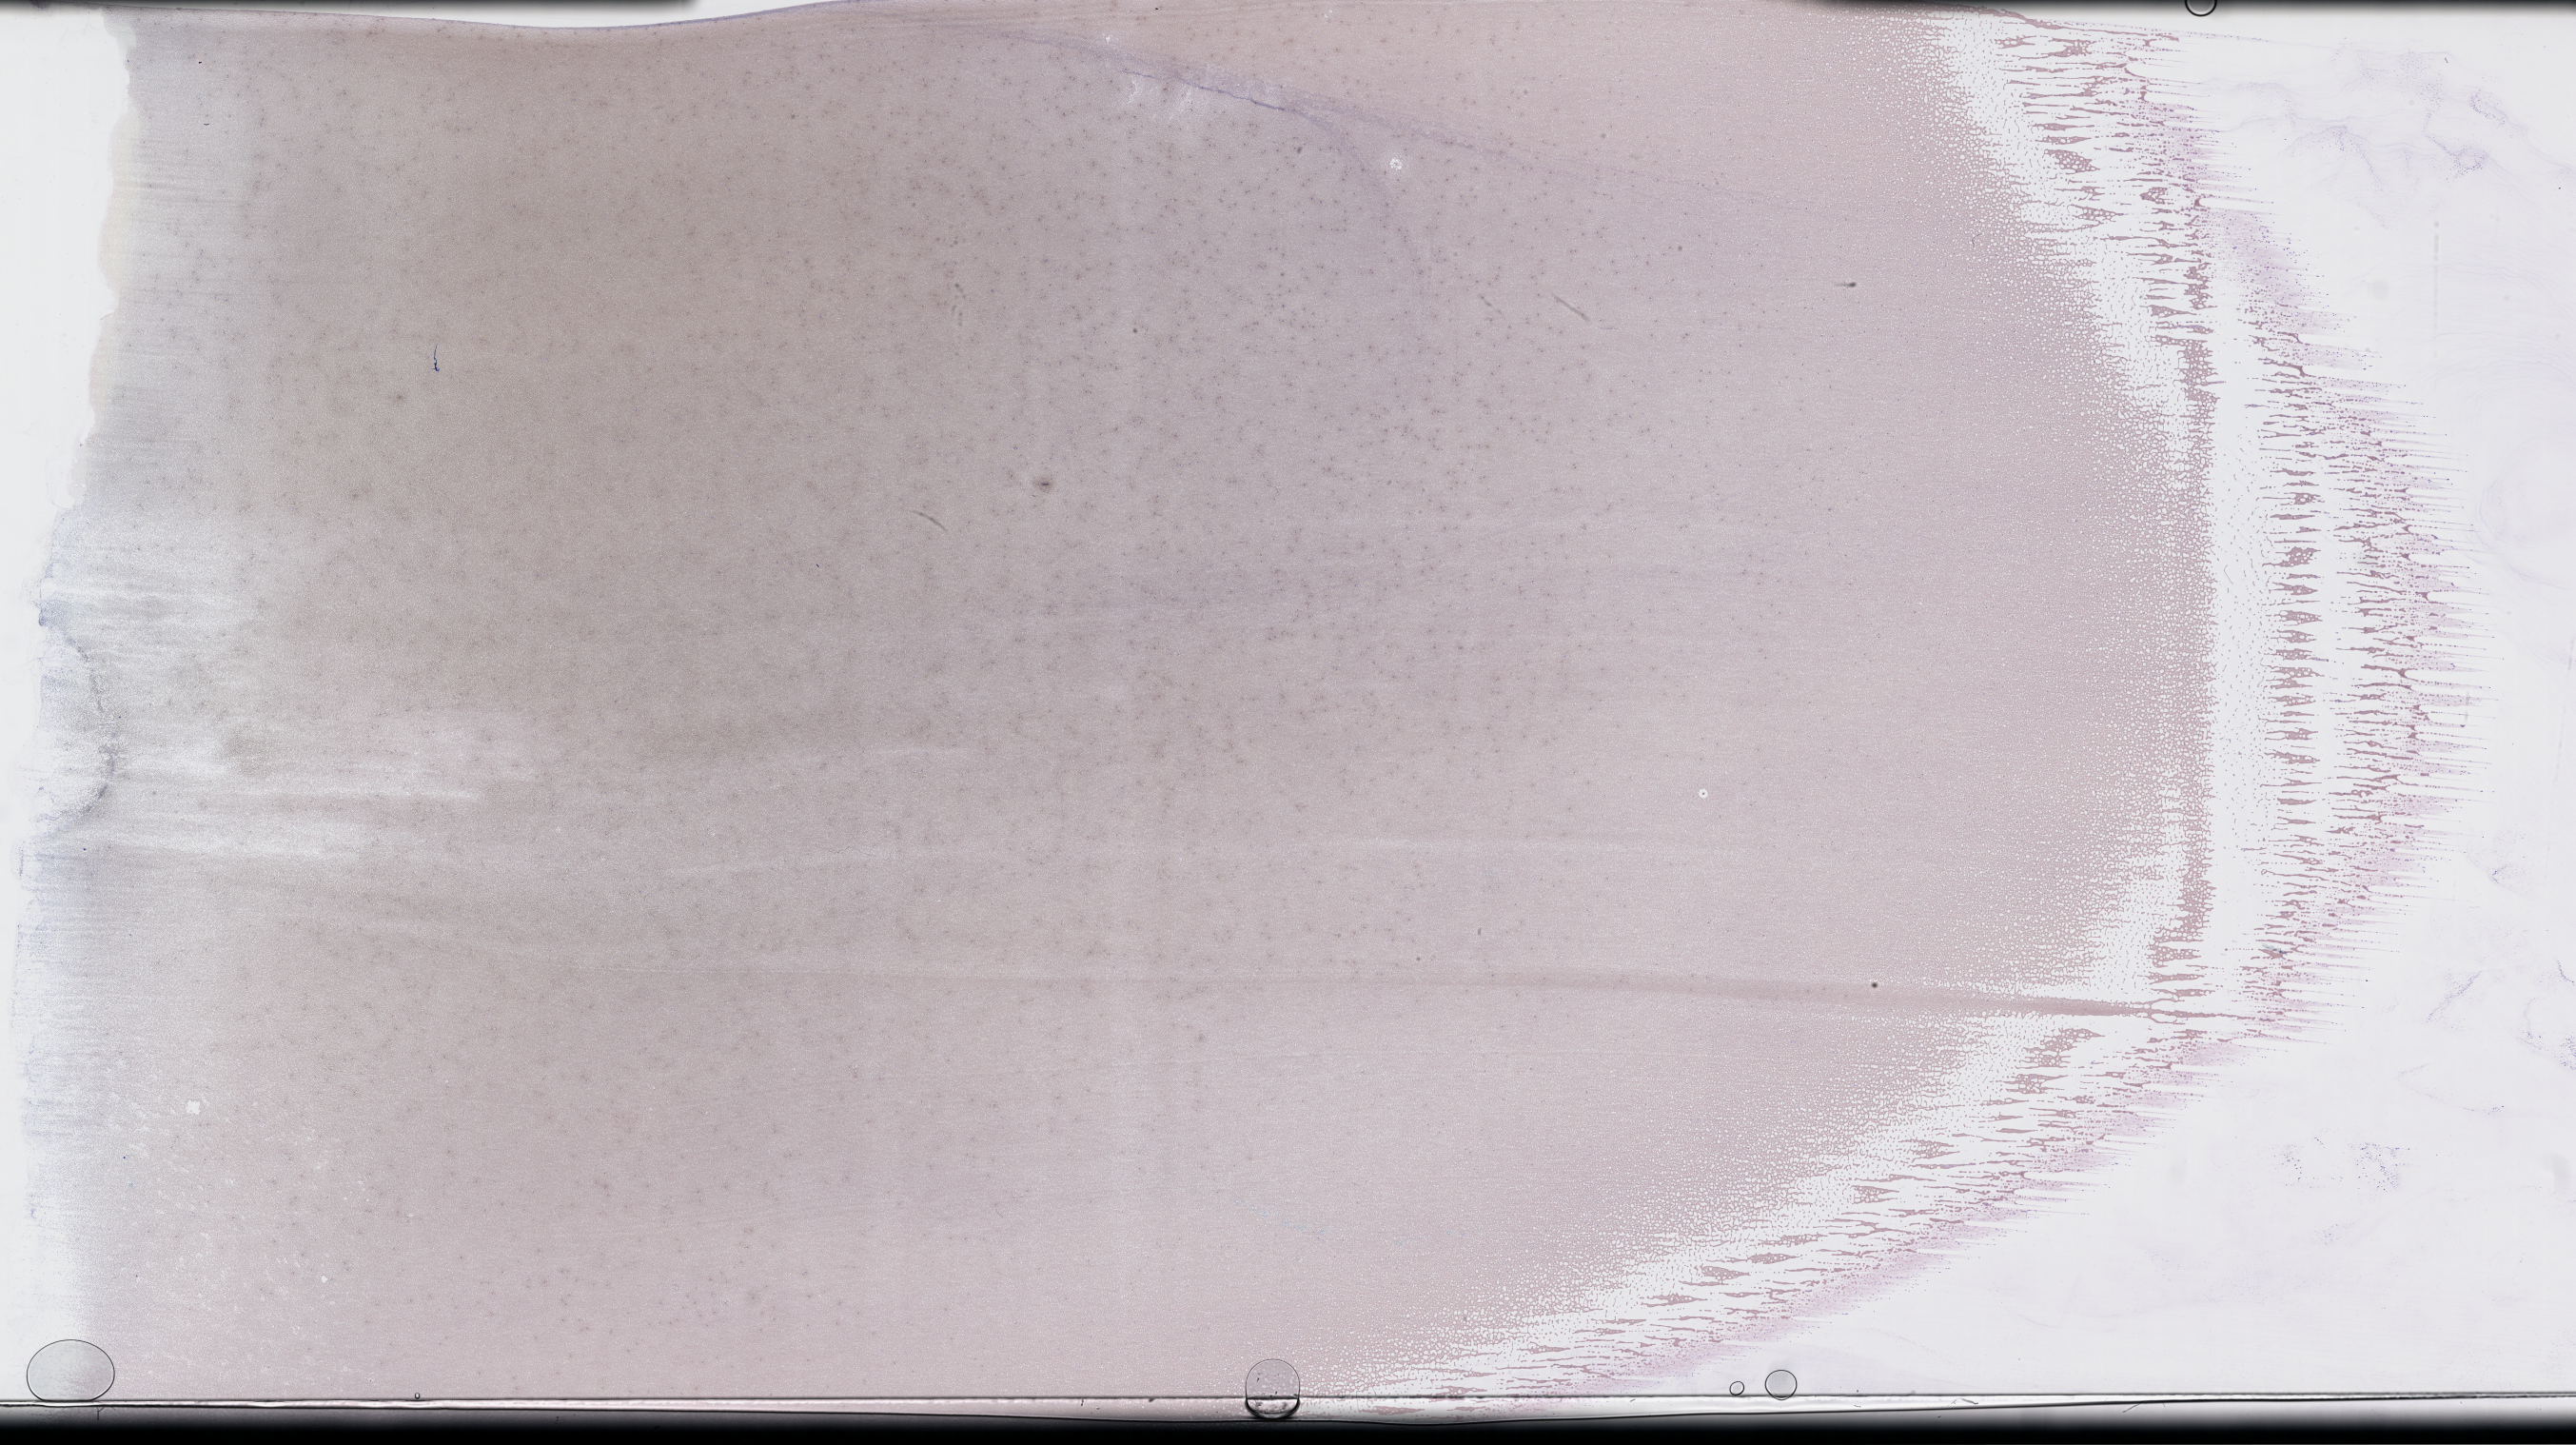
Whole-slide image of a whole blood smear, Wright–Giemsa stain — a low-resolution overview of the entire scanned area, about 43.7 x 24.5 mm, specimen time point: collected on treatment. Patient: male.
Patient diagnosis: Plasma Cell Myeloma.